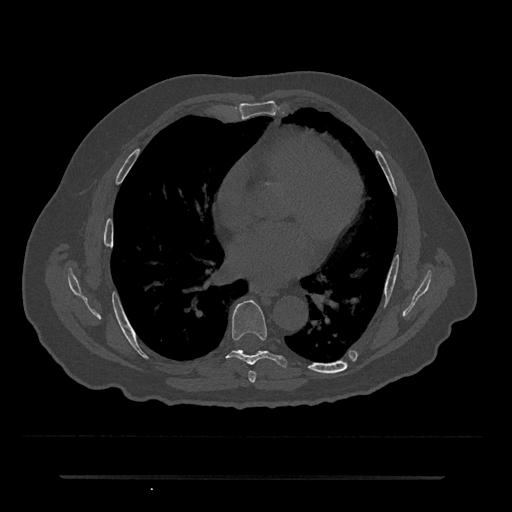
CT including the spine, one axial slice. Position 384 of 797 along the scan axis. Reconstruction kernel Br40s/3. 120 kVp. Bone window (W 1800 / L 400 HU). 0.5 mm slice thickness. 512 × 512 image matrix. Patient: male, 69 years. Case-level facts recorded for this patient, not image findings: primary cancer: prostate.
Annotated regions visible in this slice (semi-automatically segmented with operator editing):
- T6 vertebra: bounding box (x1, y1, x2, y2) in pixels: (248, 371, 256, 383)
- T7 vertebra: (227, 300, 287, 367)